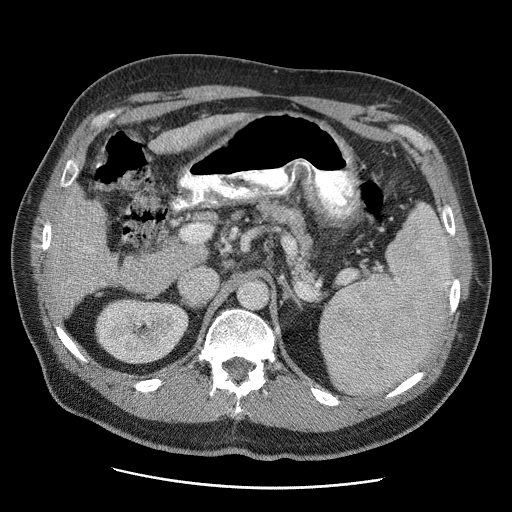
Contrast-enhanced abdominal CT (liver protocol), one axial slice; position 21 of 81 along the scan axis; soft-tissue window (W 400 / L 40 HU); 2.5 mm slice thickness; 512 × 512 image matrix, field of view 380 × 380 mm. Case-level facts recorded for this patient, not image findings: diagnosis: hepatocellular carcinoma (patient treated with transarterial chemoembolisation; whether this scan precedes or follows treatment is not stated here); TNM stage (as recorded): Stage-IIIA; Child-Pugh class: A; tumour nodularity: multinodular; tumour size: 5.5 cm.
Structures marked on this image (semi-automatically segmented with operator editing):
- liver parenchyma outside the tumour (the mass and vessels are separate outlines, so this box may not span the whole liver): bounding box <50,112,248,314> (left, top, right, bottom; pixels)